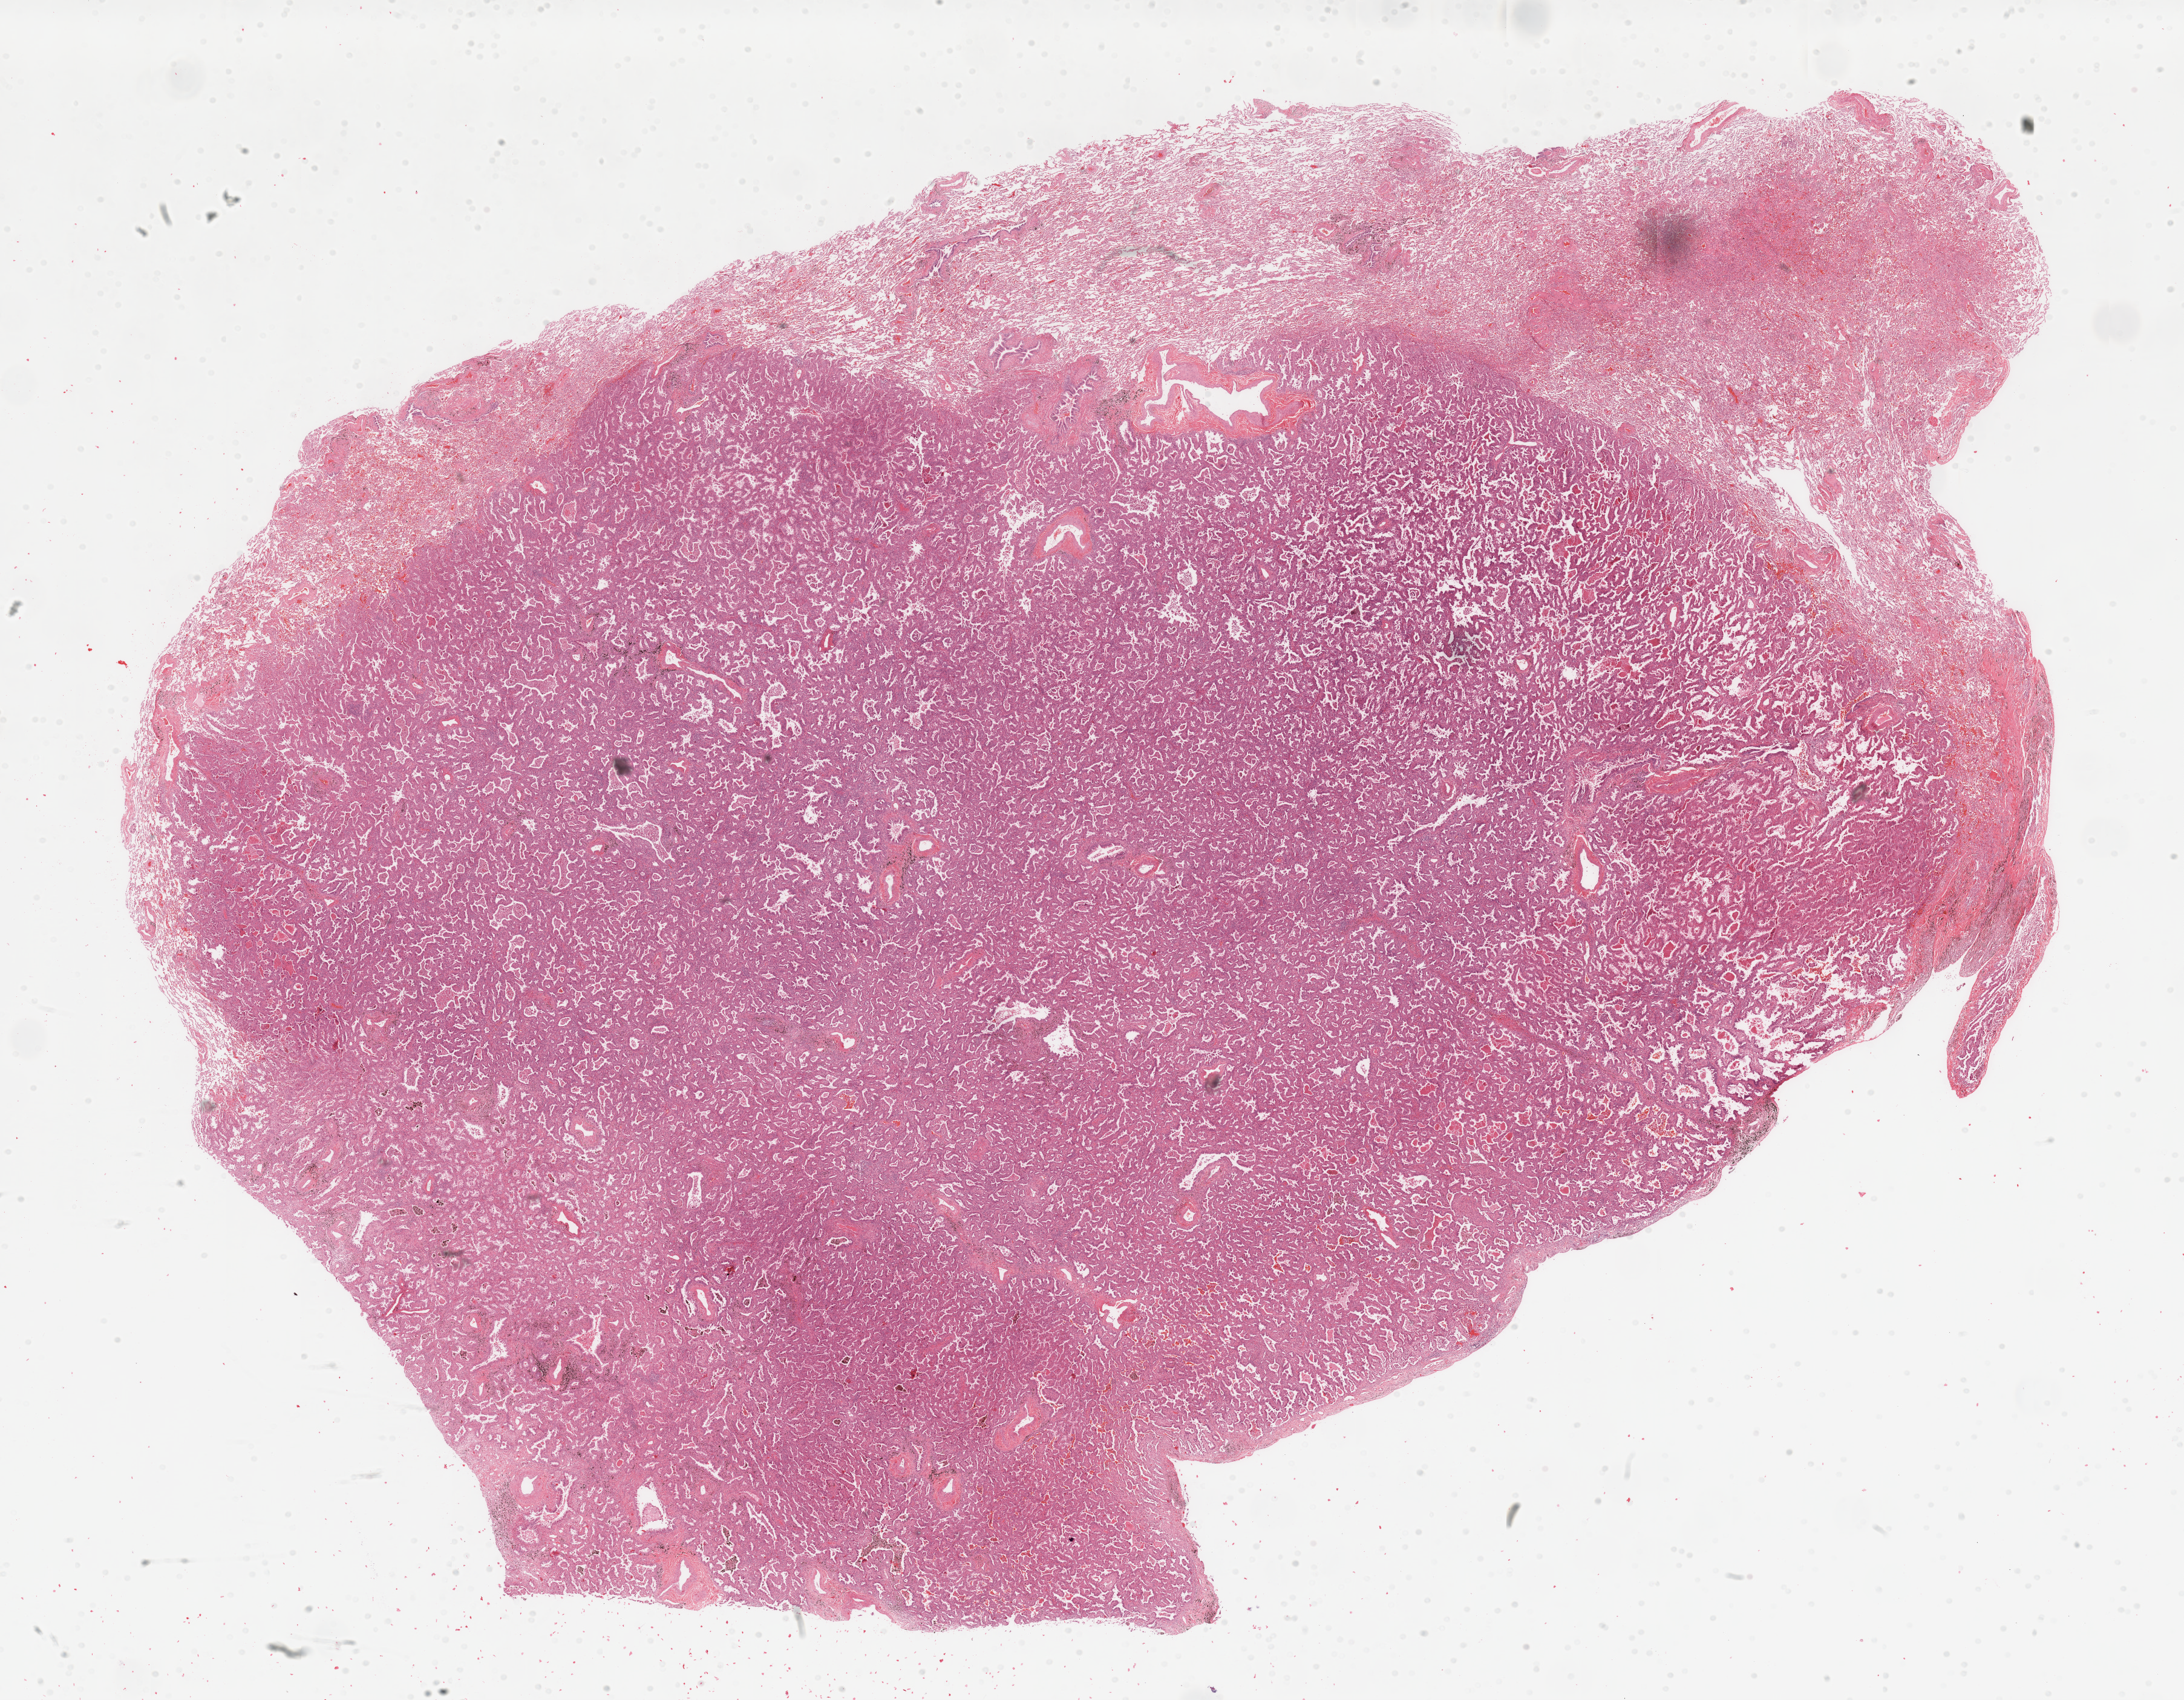
Whole-slide histology image, H&E — low-resolution overview of the scanned area, about 28.5 x 22.2 mm (from a 20x scan). Lung, tumour tissue. Patient: male, age 64 years. Histologic grade: G2 (moderately differentiated).
• AJCC pathologic stage: IIA
• diagnosis: Adenocarcinoma, NOS
• primary tumour site (as recorded): right lower lobe